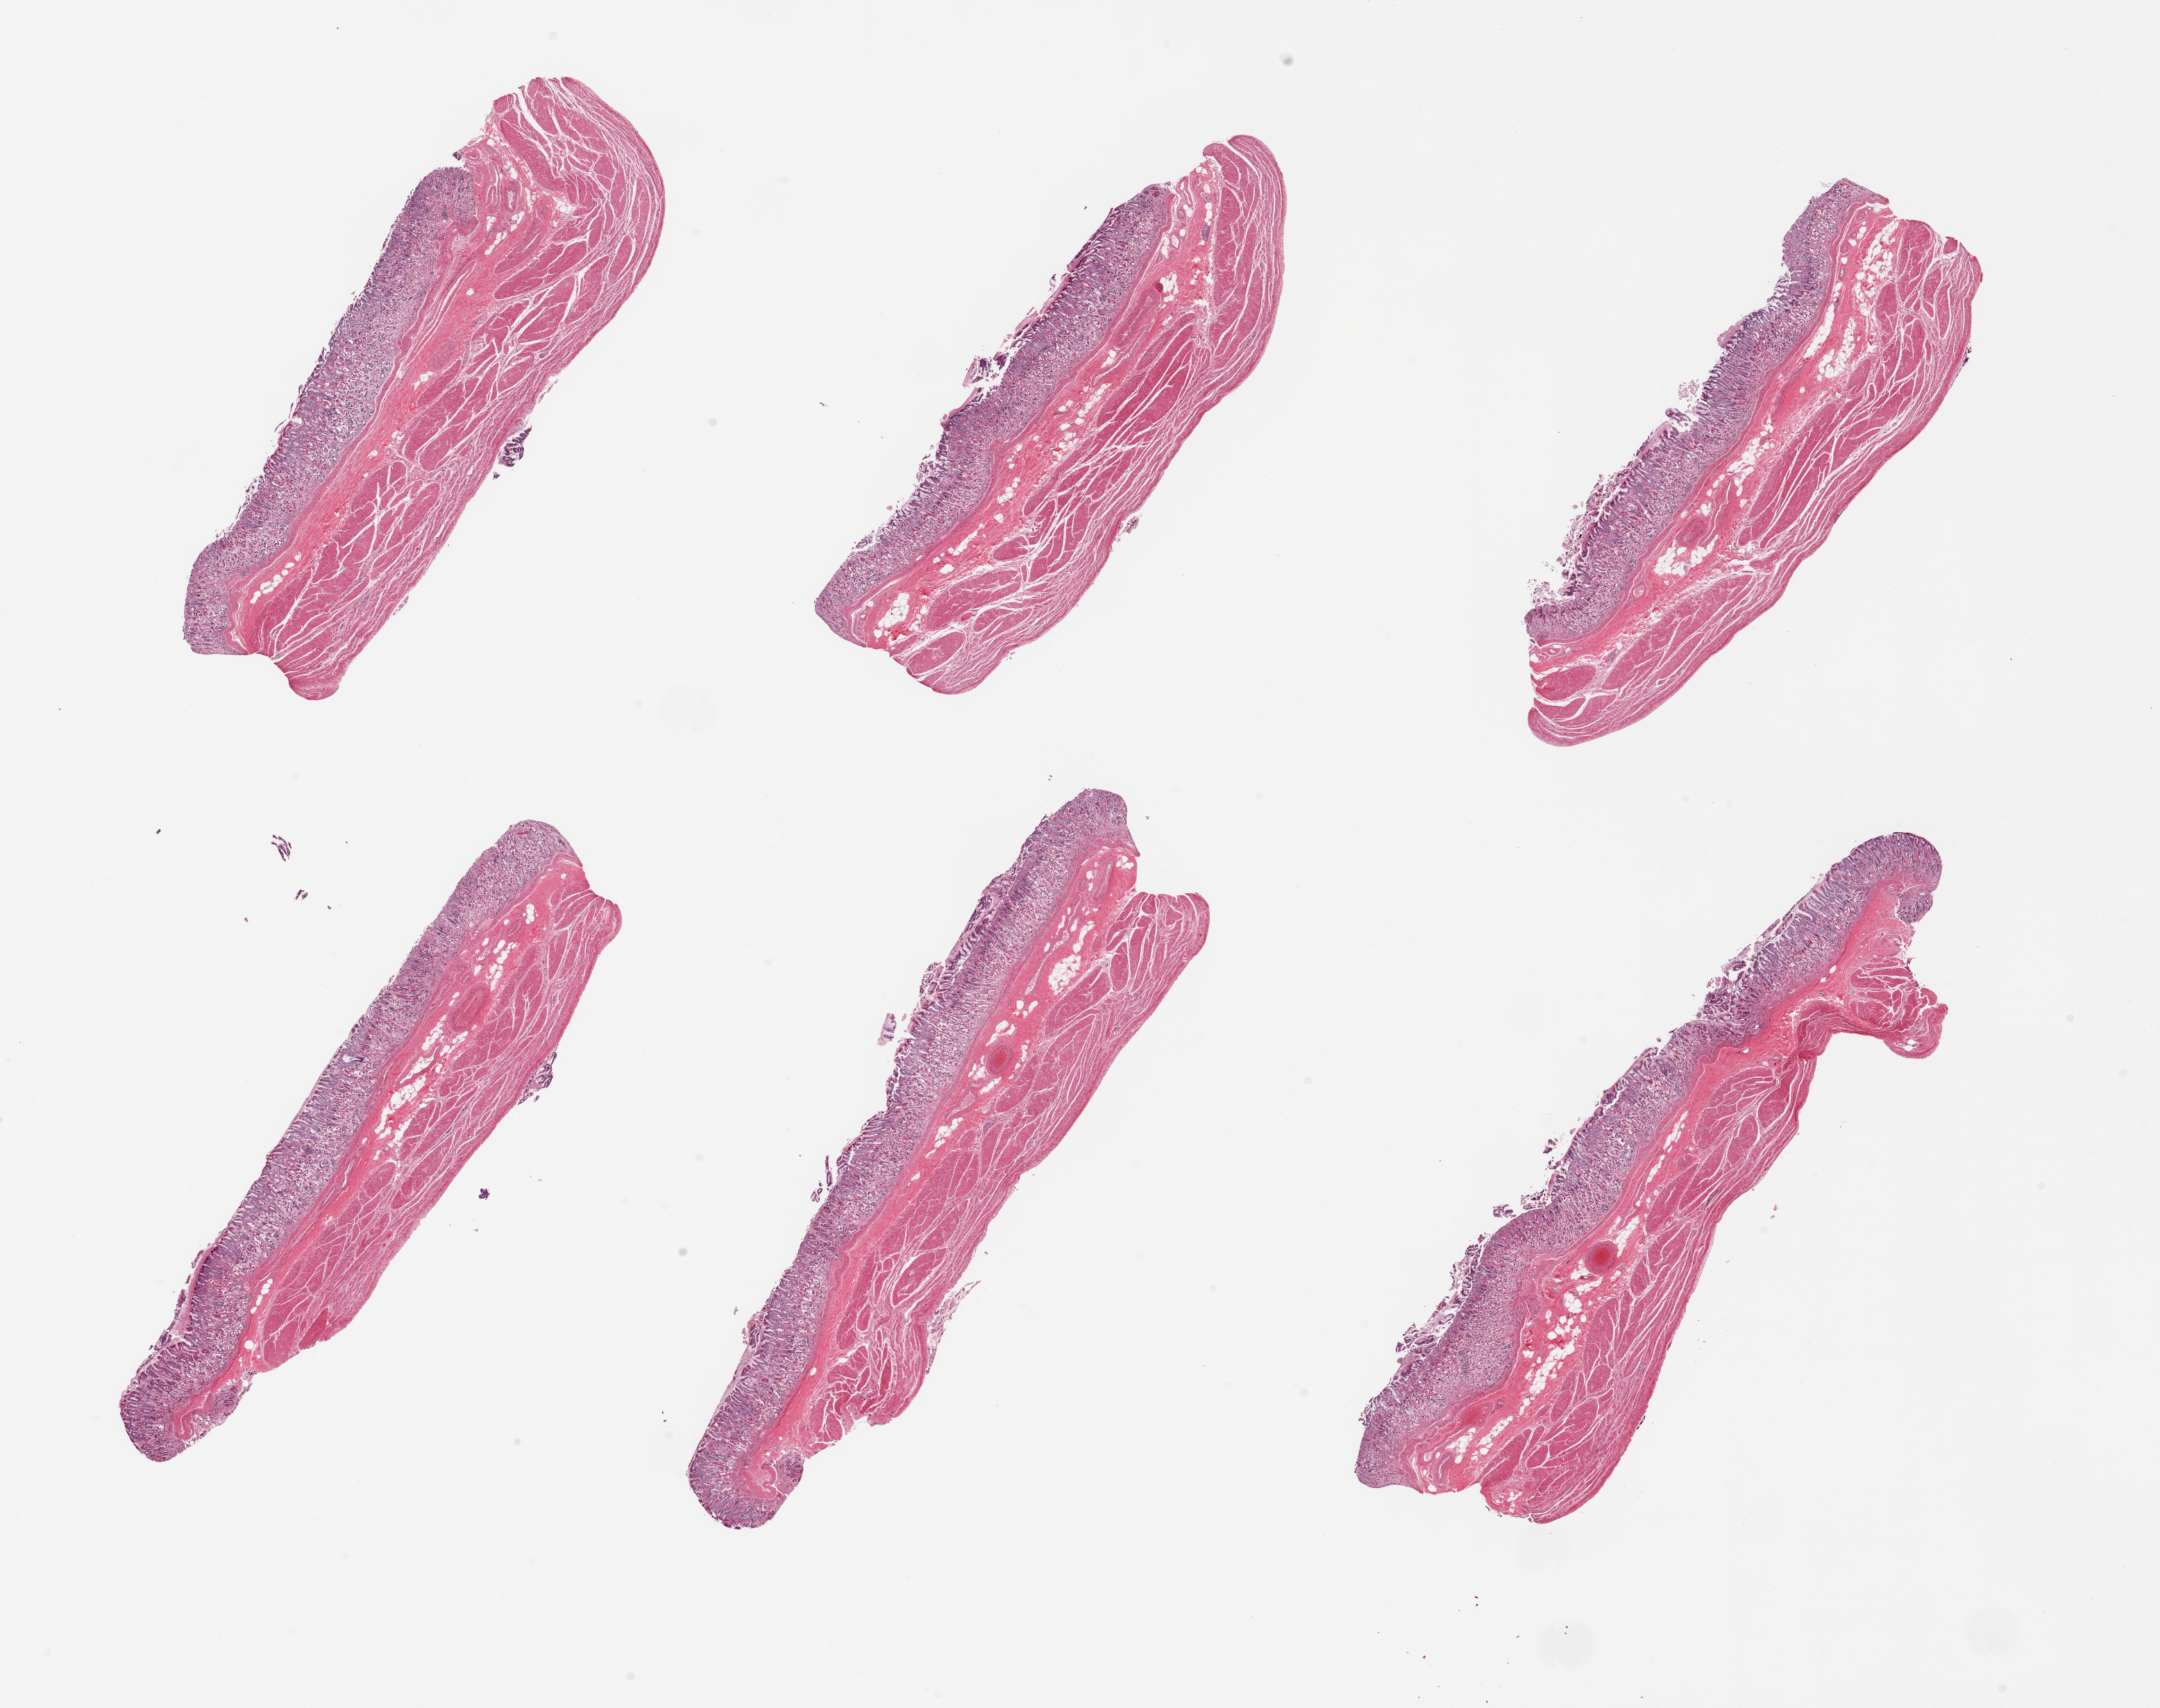
Haematoxylin and eosin whole-slide image, low-resolution overview of the scanned area, about 24.6 x 19.5 mm (from a 20x scan); PAXgene-fixed, paraffin-embedded tissue; sampled site (target tissue): stomach; tissue donor sample. Donor: male.
* pathologist's review note for this sample: 6 pieces; full thickness sections with mucosa up to 0.8mm, sloughing surface epithelium, moderate autolysis